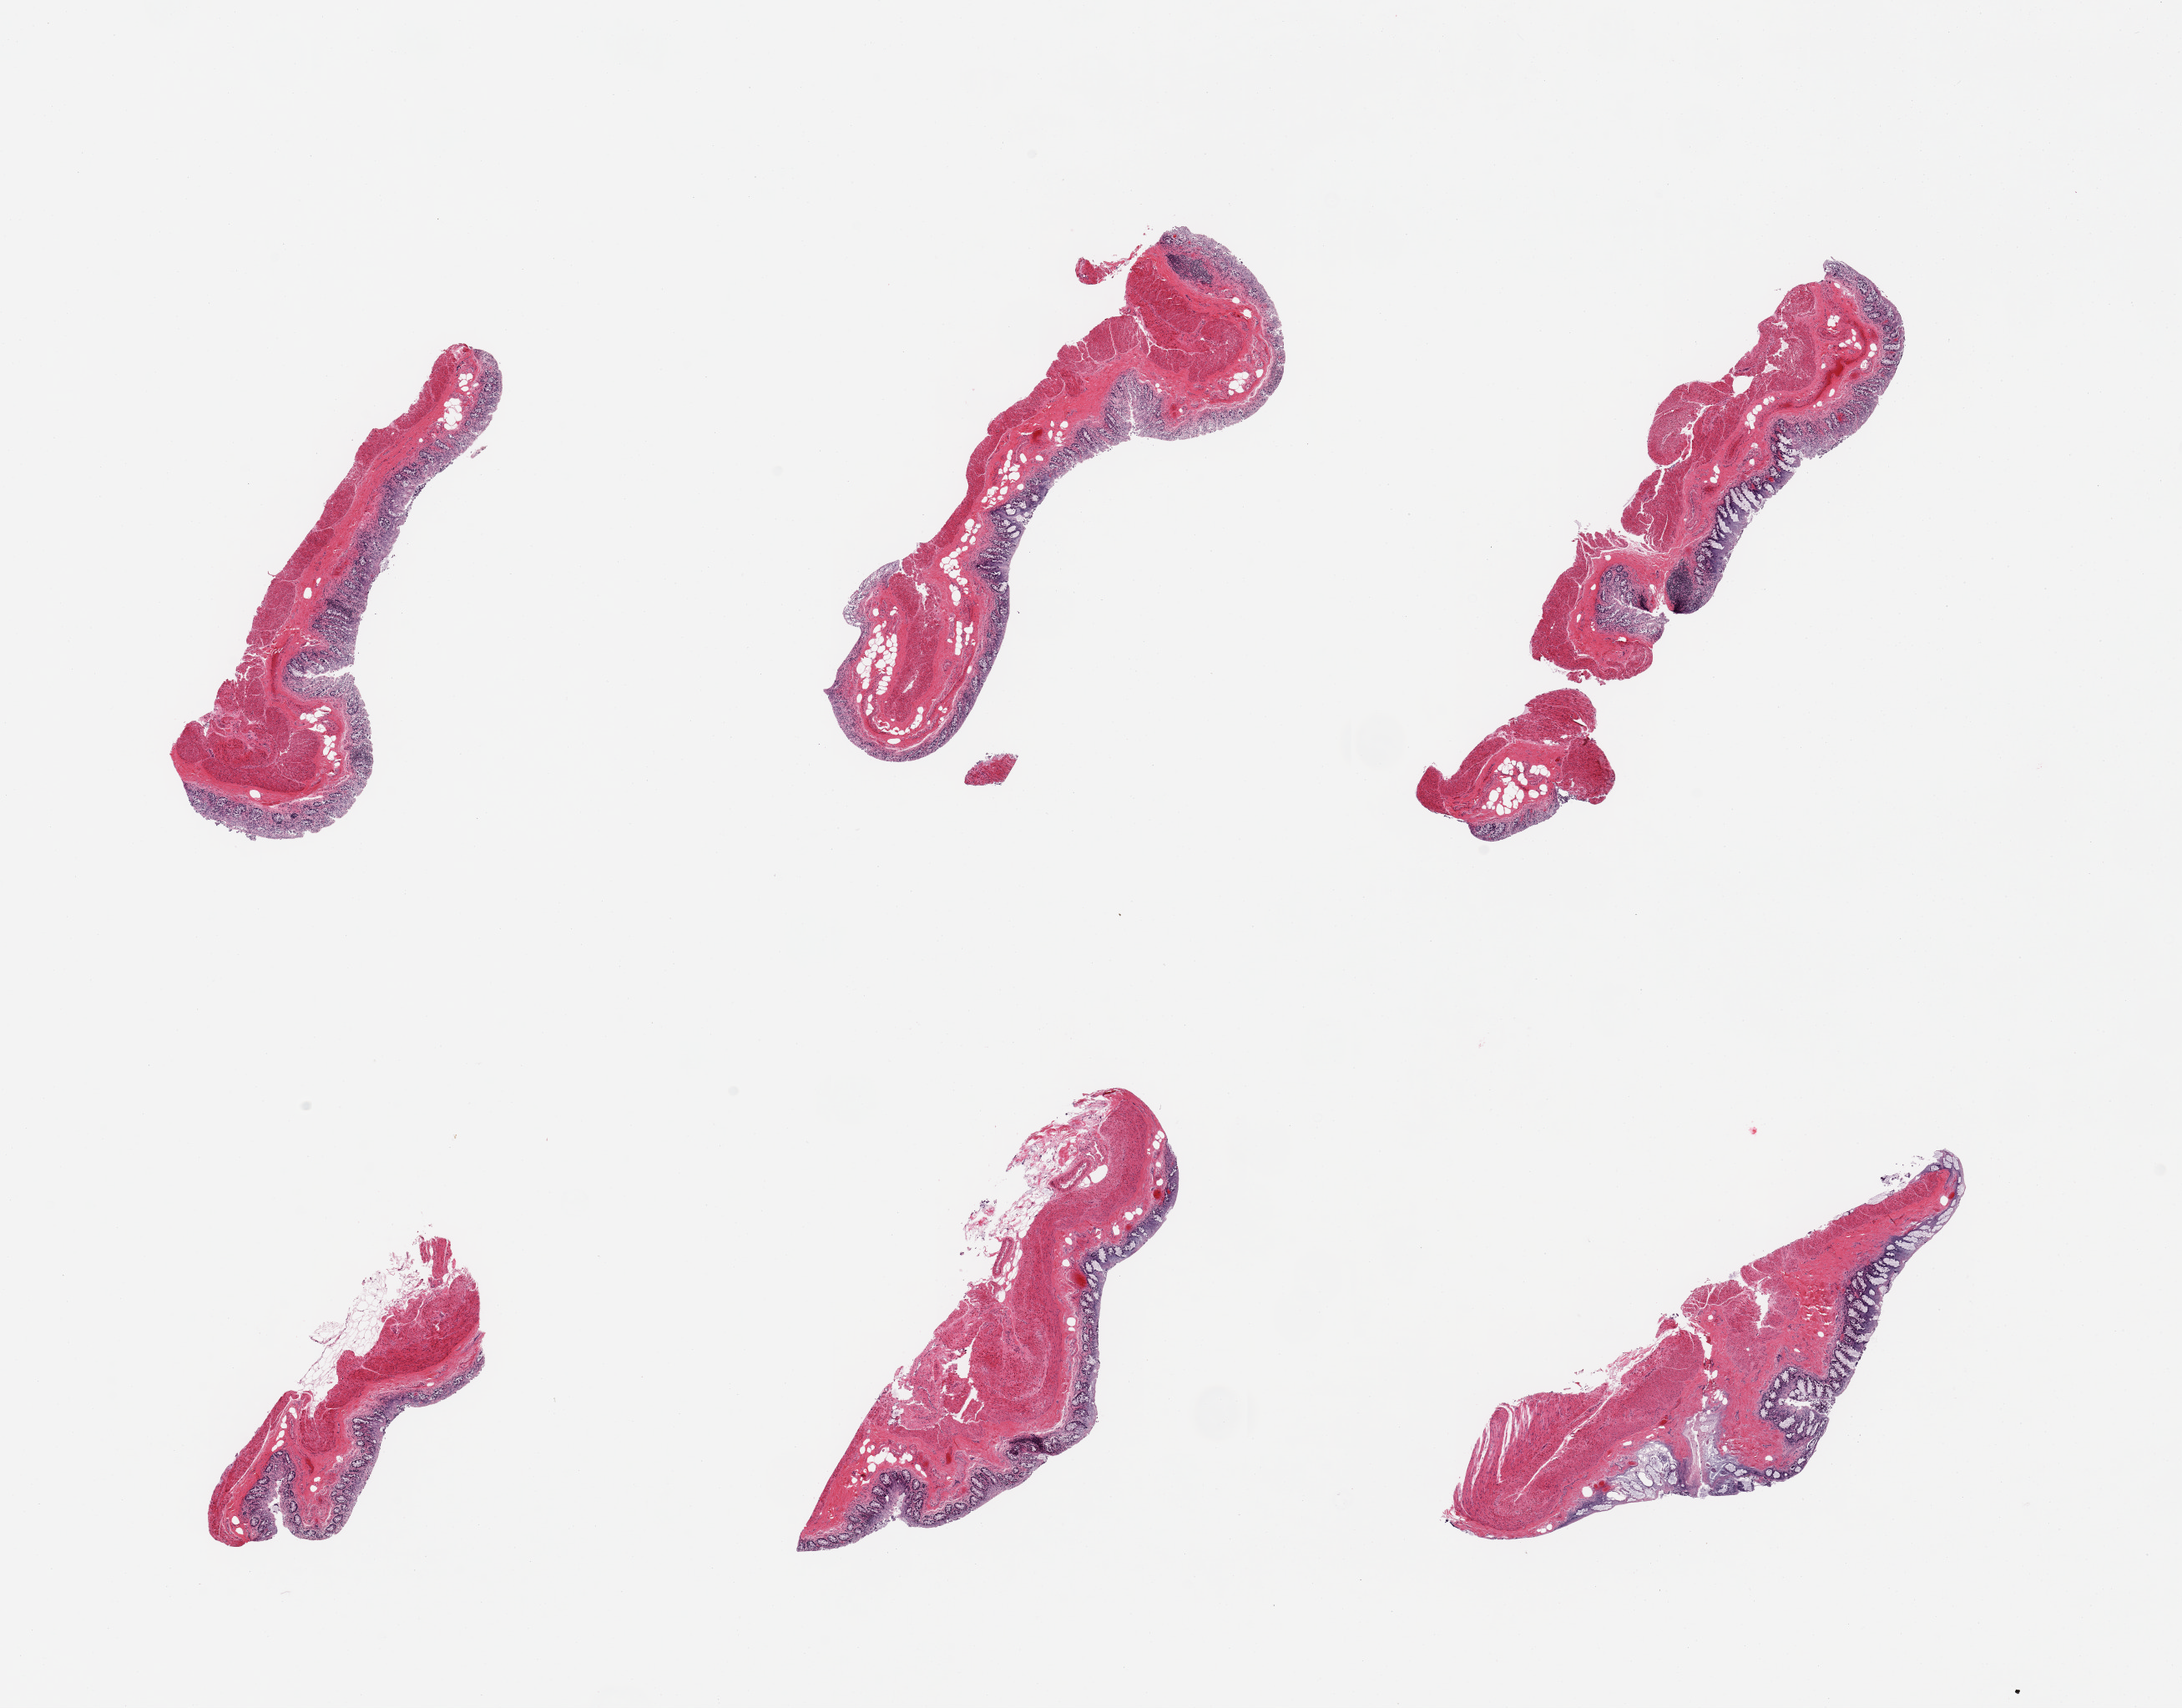
H&E whole-slide image, brightfield — low-resolution overview of the scanned area, about 20.7 x 16.2 mm (slide scanned at 20x); PAXgene-fixed, paraffin-embedded tissue; target tissue: transverse colon; tissue donor sample. Donor sex: male.
Reviewer comment on this tissue sample: 6 pieces; some deeper glands are better preserved than the rest.